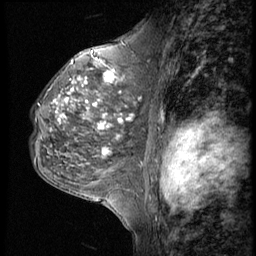
Breast MRI (dynamic contrast-enhanced), one sagittal slice. Slice 31 of 56 in the series (ordered by position). 4 images stored at this slice position (order not interpretable as contrast timing). 1.5 T. TE 4.2 ms, TR 9 ms. 2.5 mm slice thickness. 256 × 256 image matrix. Female patient, age 50 years. Case-level facts recorded for this patient, not image findings: setting: breast cancer imaged before/during neoadjuvant chemotherapy; receptor status: triple-negative.
Annotated regions visible in this slice (semi-automatic segmentation, software-assisted and operator-edited):
- analysis volume of interest (the breast-tissue region the enhancement analysis was run in; not a lesion): bounding box [x1, y1, x2, y2] px = [29, 46, 148, 188]
- tumour enhancement mask (voxels above the 140 % enhancement threshold inside the analysis volume of interest): [56, 71, 132, 155]